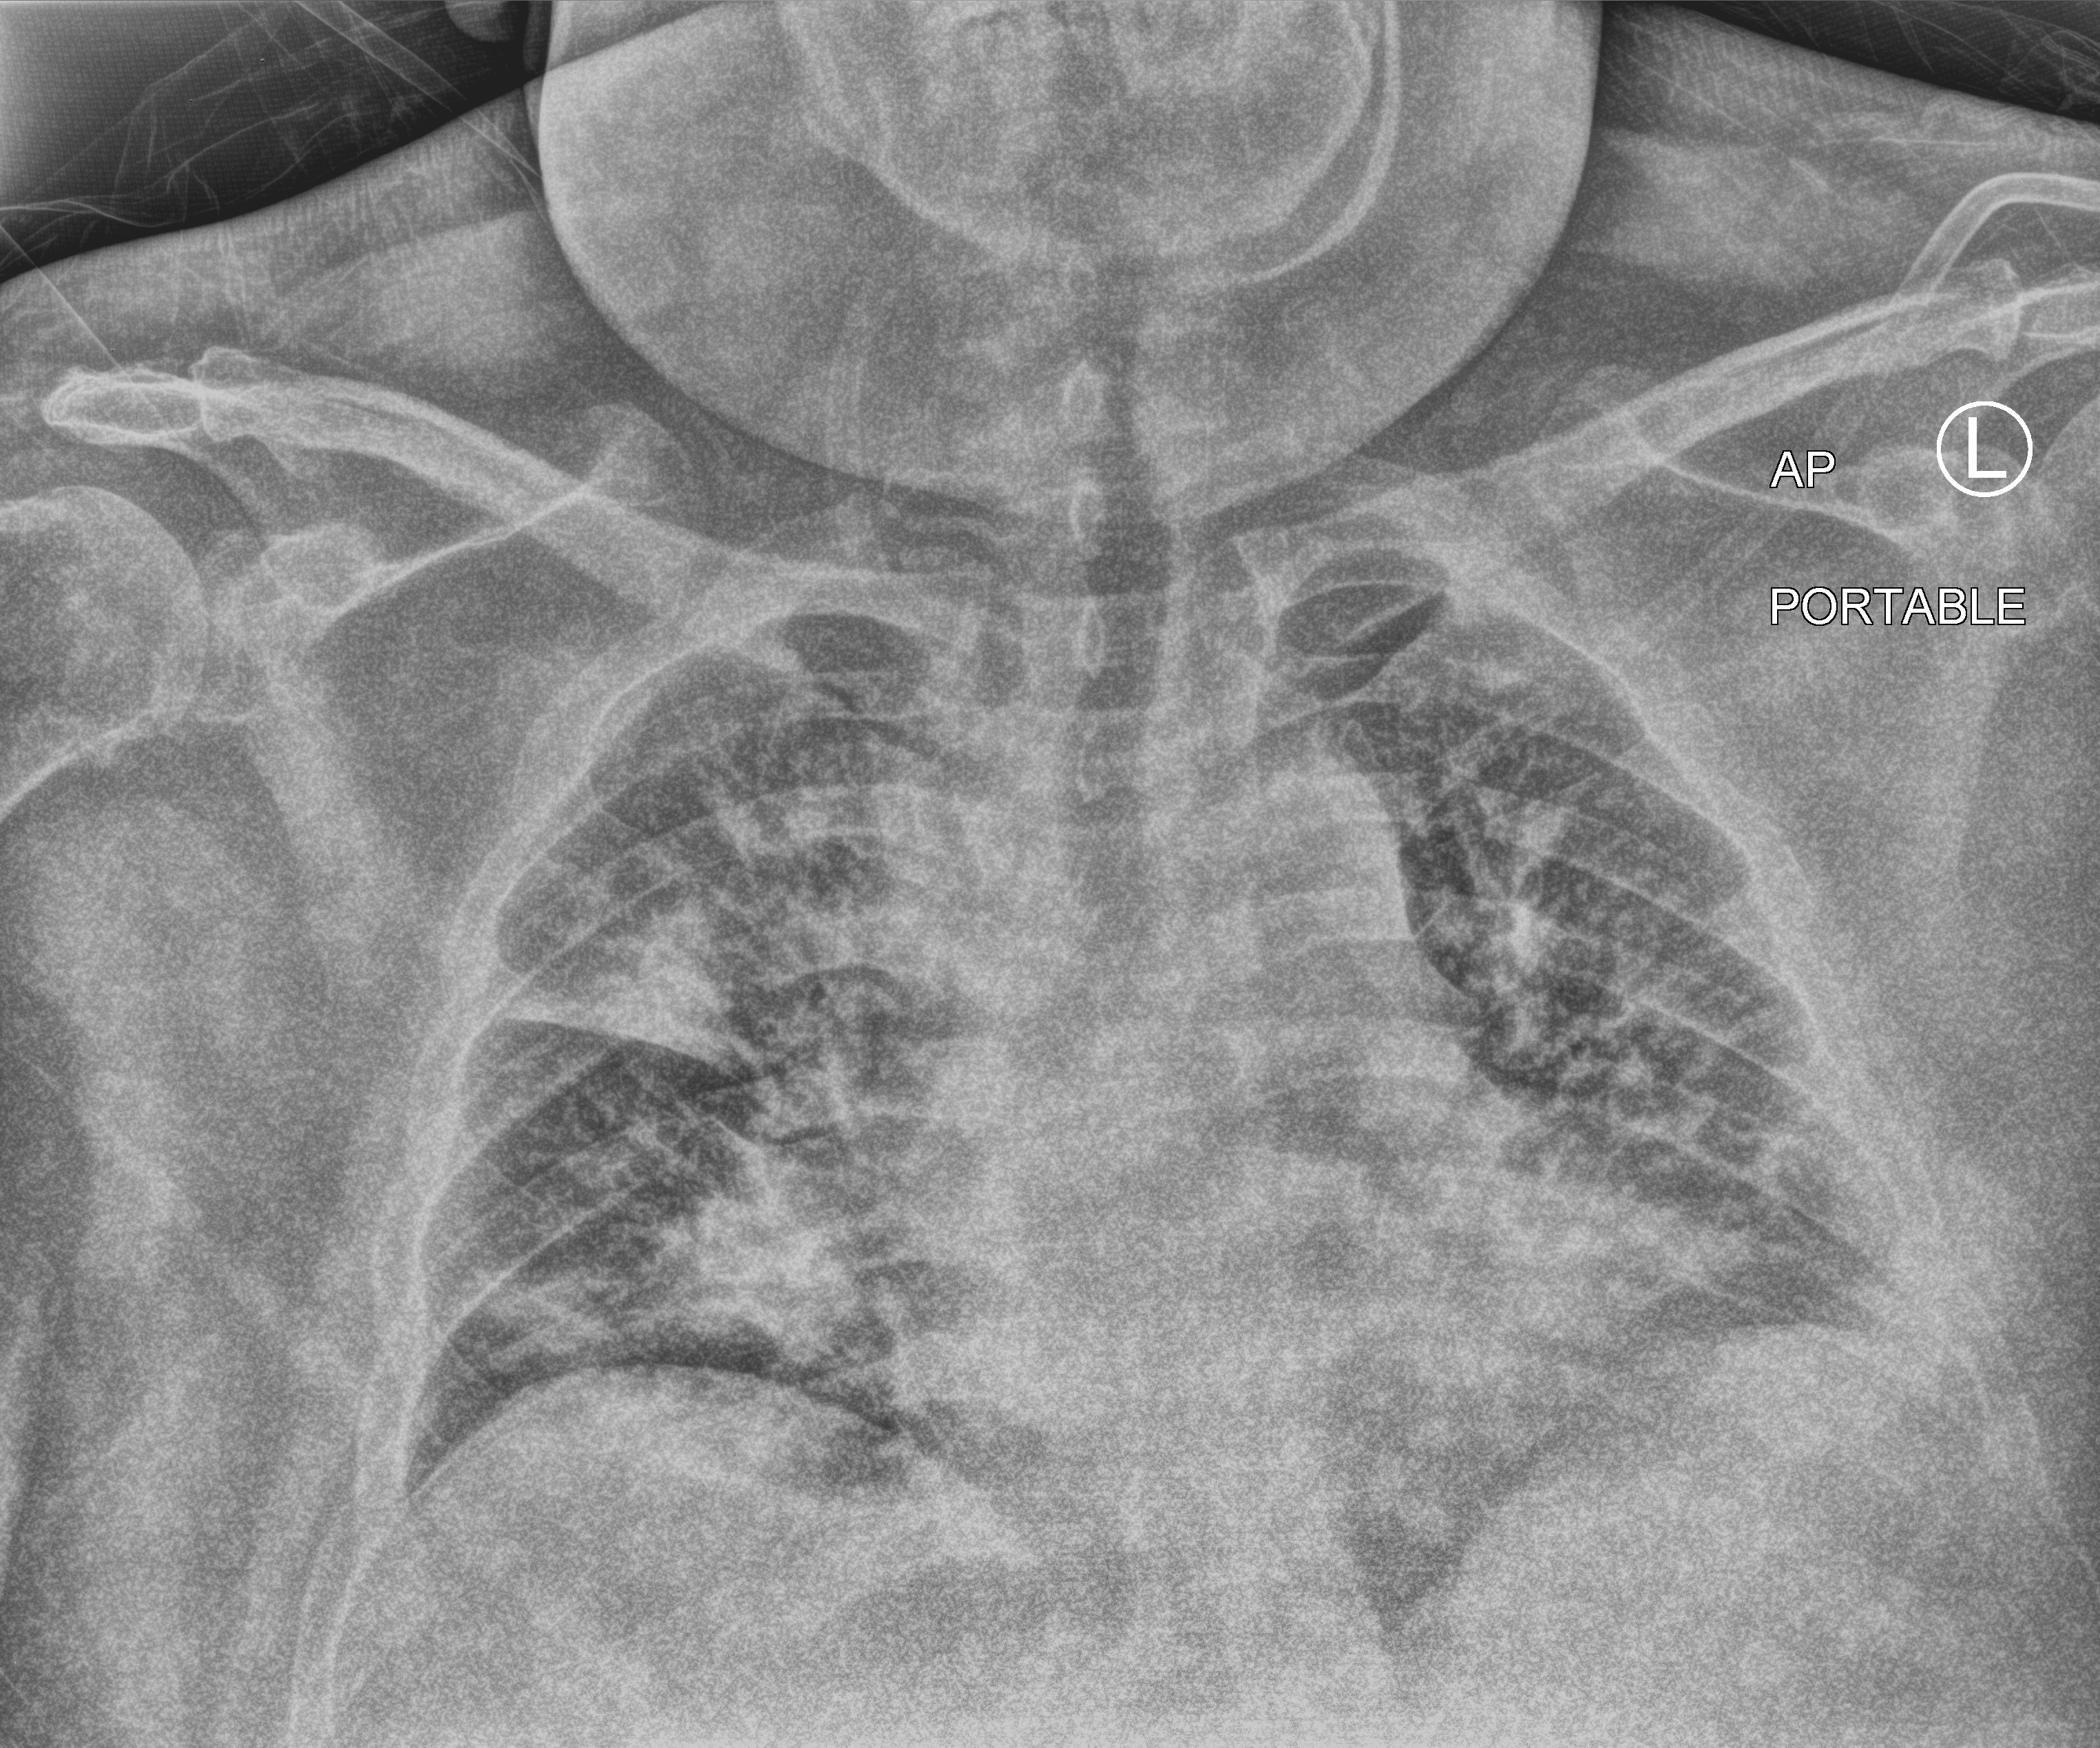
Chest X-ray (portable). Male patient hospitalised with COVID-19, age 18–59 years.
From the hospital-stay record, not from the radiograph (when in the stay this image was taken is not recorded):
- mechanically ventilated during this hospital stay: no